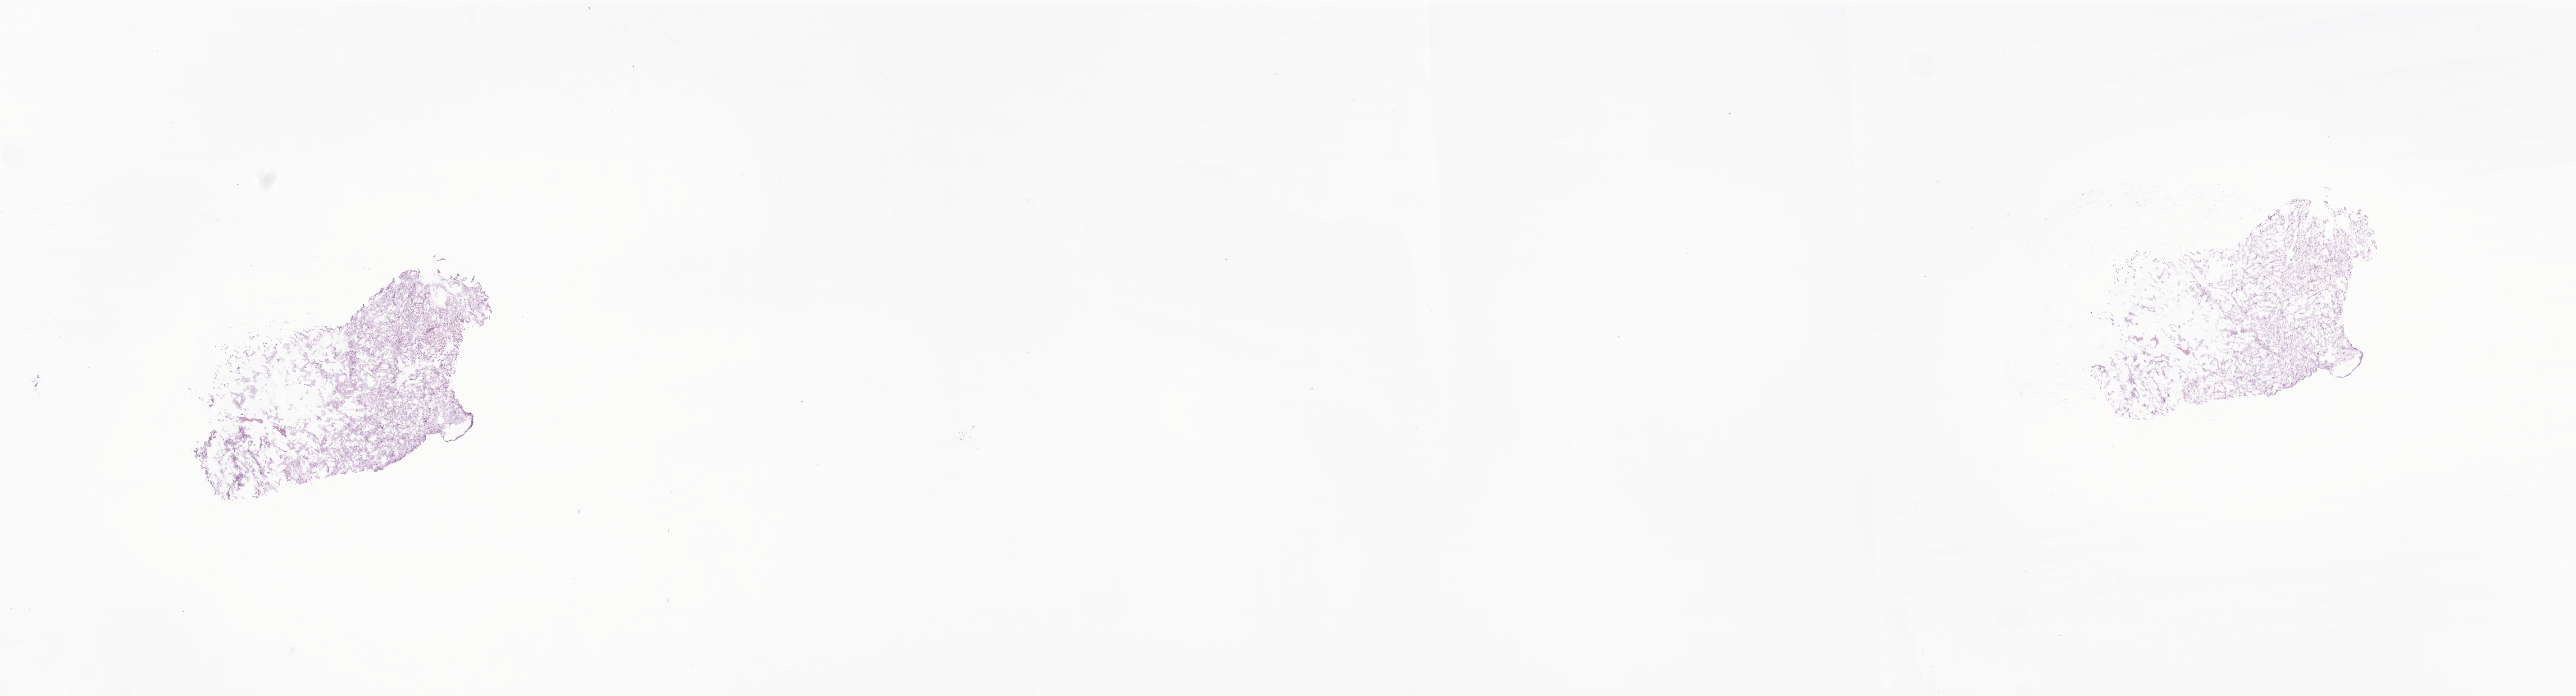
Digitized hematoxylin and eosin (H&E)-stained section of tumor tissue from the cerebellum — a low-resolution overview of the entire scanned area, about 24.1 x 6.5 mm; cryosection (OCT / tissue freezing medium). Patient male; age 92 months (7 years 8 months).
• diagnosis (ICD-O-3 morphology term): Pilocytic astrocytoma